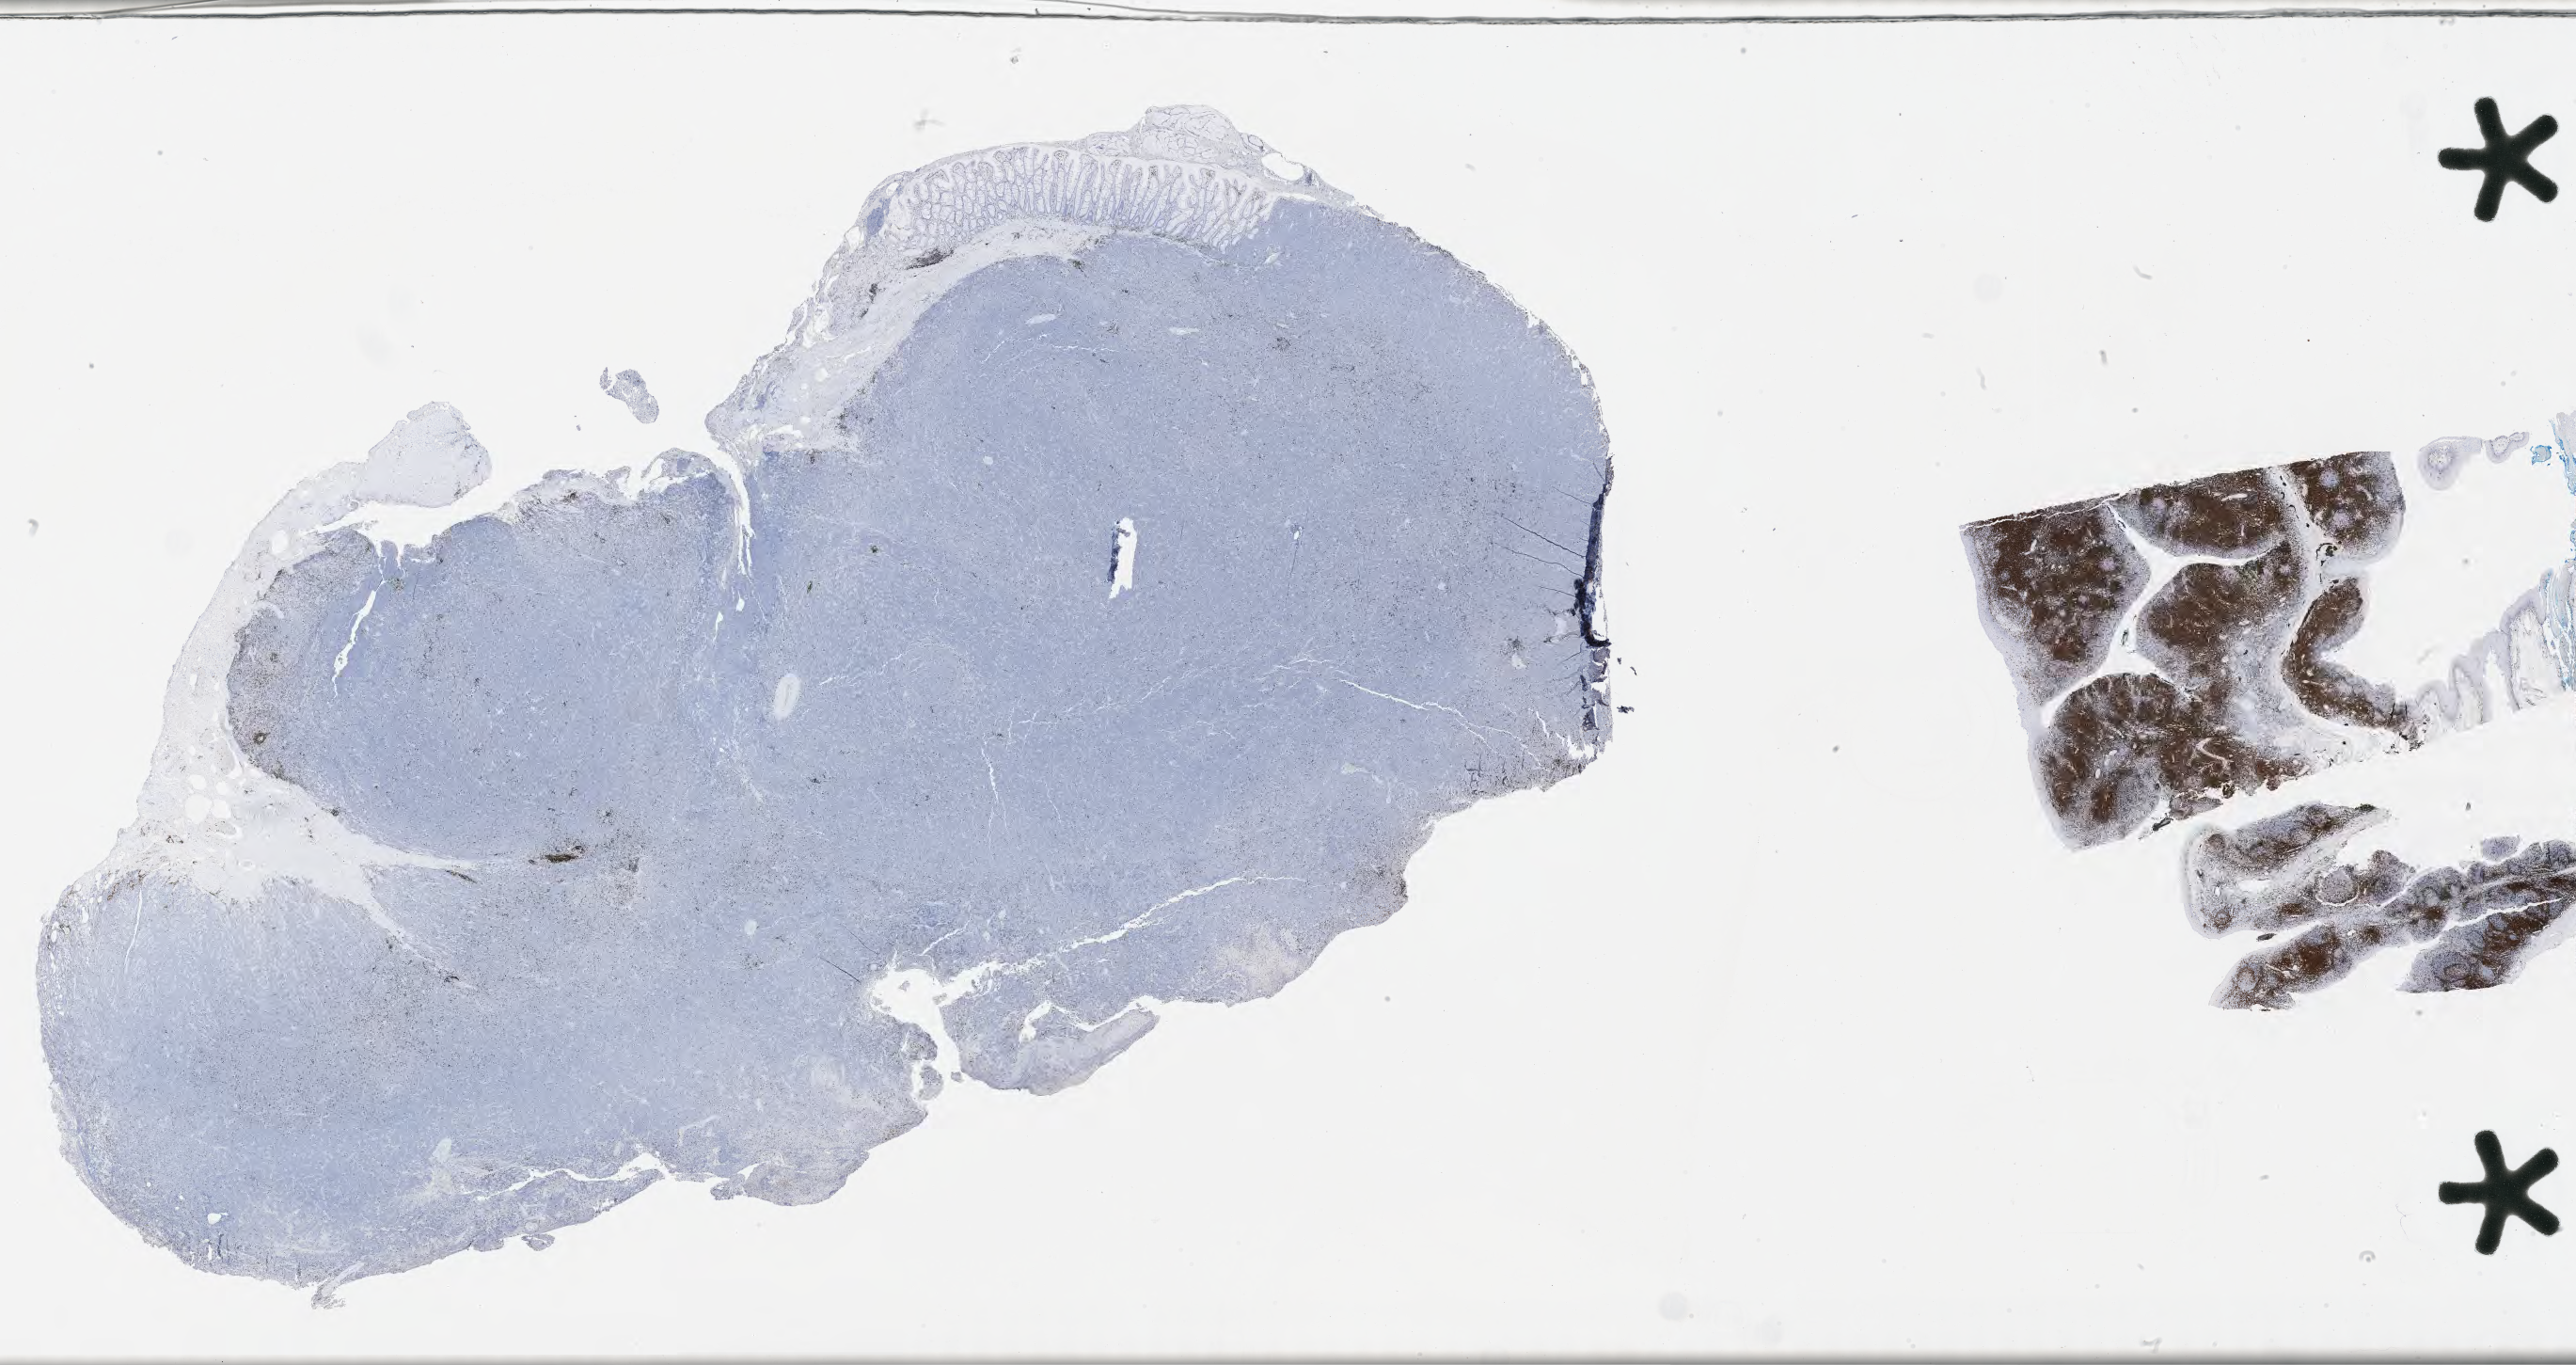
IHC for CD3, whole-slide image — shown as a low-resolution overview of the whole scanned area (about 44.3 x 23.4 mm). Tumor tissue. Female patient, aged 29.
Diagnosis: Burkitt lymphoma, NOS.